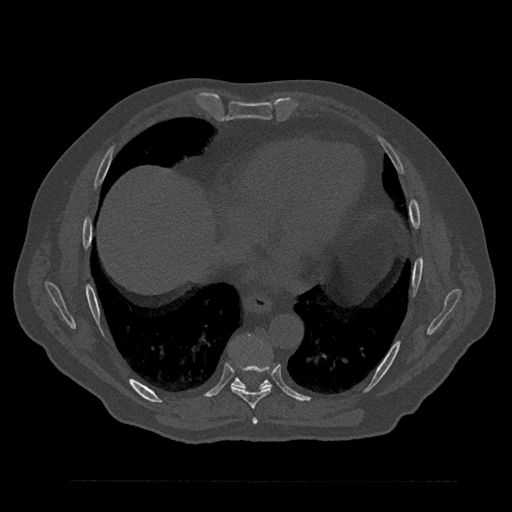
CT including the spine, one axial slice; slice 438 of 797 in the series (ordered by position); reconstruction kernel Br40s/3; bone window (W 1800 / L 400 HU); 0.5 mm slice thickness; 512 × 512 image matrix, field of view 430 × 430 mm. Male patient, age 61 years. From the clinical record (not read from this slice): primary cancer: prostate.
Annotated regions visible in this slice (semi-automatically segmented with operator editing):
- T7 vertebra: bounding box [x1, y1, x2, y2] px = [252, 418, 258, 424]
- T8 vertebra: [230, 365, 272, 409]
- T9 vertebra: [231, 335, 272, 389]